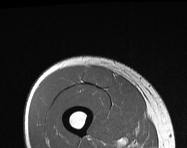
MRI of an extremity soft-tissue mass, one axial slice; position 42 of 114 along the scan axis; MR volume resampled by the dataset authors to the PET/CT grid (not the native acquisition matrix); 3.27 mm slice thickness; 187 × 148 image matrix, field of view 183 × 145 mm. Male patient. Case-level facts recorded for this patient, not image findings: histological type: pleiomorphic leiomyosarcoma; grade: intermediate; site of the primary tumour: right thigh.
Structures marked on this image (expert contour drawn on MRI and transferred to this co-registered scan by the dataset authors):
- gross tumour volume including surrounding oedema: box from (x=84, y=66) to (x=112, y=87) px